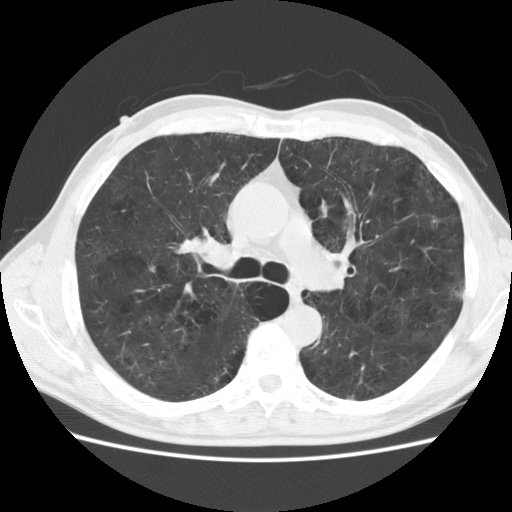
Chest CT (low-dose screening protocol), one axial image, baseline annual screen, lung window (W 1500 / L -600 HU), 2.5 mm slice thickness, slice 70 of 177 in the series, 512 × 512 image matrix. Male, age 58 years at enrolment. Current smoker at enrolment.
• Expert reader's lesion annotation, box from (x=415, y=202) to (x=456, y=243) px.
• No non-calcified nodule or mass ≥4 mm was recorded by the screening reader at this exam.
• Later outcome: lung cancer diagnosed 832 days after this screen (after the third annual screen) — adenocarcinoma, NOS, left upper lobe, stage IA (AJCC 6th edition), 9 mm at pathology.